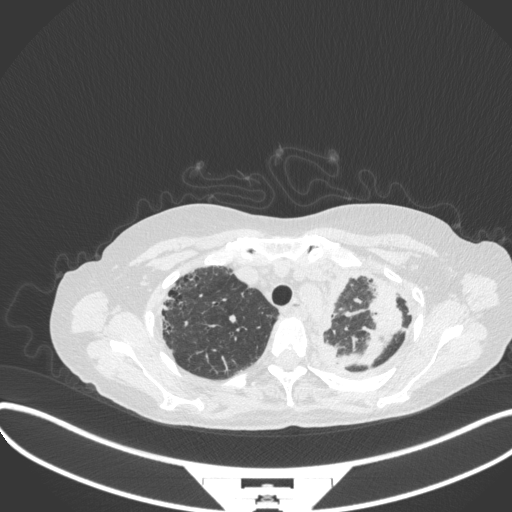
Chest CT, one axial slice; slice 278 of 373 in the series (ordered by position); reconstruction kernel B31f; 120 kVp; lung window (W 1500 / L -600 HU); 1 mm slice thickness; 512 × 512 image matrix, field of view 400 × 400 mm. Female patient, age 56 years. Case-level facts recorded for this patient, not image findings: clinical TNM (as recorded): T1 N0 M0.
Outlined on this slice (rectangle marked by the reading radiologist):
- lung tumour (recorded histology: adenocarcinoma): bounding box <340,277,406,368> (left, top, right, bottom; pixels)